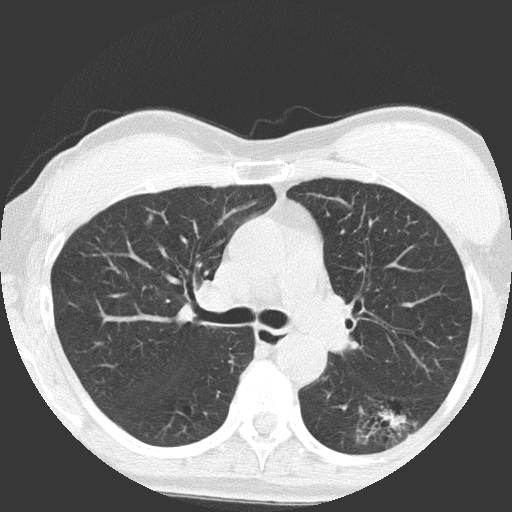
Chest CT (low-dose screening protocol), one axial image. Baseline annual screen. Lung window (W 1500 / L -600 HU). 2 mm slice thickness. Female, age 64 years at enrolment.
Expert-annotated lung lesion, bounding box [x1, y1, x2, y2] px = [340, 390, 427, 462]. Screening reader's record for this exam (one nodule recorded; not confirmed to be the boxed lesion): non-calcified nodule or mass ≥4 mm, right upper lobe, 4 × 4 mm, poorly defined margins, ground glass attenuation. Note: the box lies in the patient's left hemithorax on this image, whereas the reader's record names the right lung; they may be different findings. Lung cancer was diagnosed 932 days after this screen: adenocarcinoma, NOS, left lower lobe, moderately differentiated (G2), stage IA (AJCC 6th edition), 17 mm at pathology.